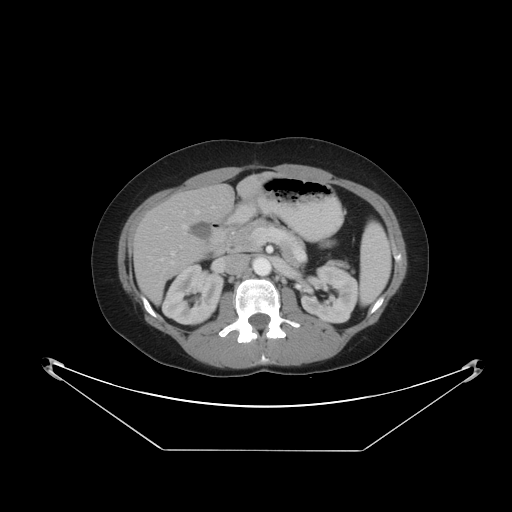
Contrast-enhanced abdominal CT, one axial slice. Position 22 of 48 along the scan axis. Soft-tissue window (W 400 / L 40 HU). 5 mm slice thickness. 512 × 512 image matrix. Female patient, age 38 years. From the clinical record (not read from this slice): diagnosis: colorectal cancer liver metastases, imaged before liver resection.
Annotated regions visible in this slice (outlined manually by an expert reader):
- hepatic veins: bounding box <182,210,198,229> (left, top, right, bottom; pixels)
- liver: <133,177,262,300>
- planned liver remnant (the part of the liver to remain after resection): <168,178,262,223>
- portal vein (with intrahepatic branches): <160,206,214,264>